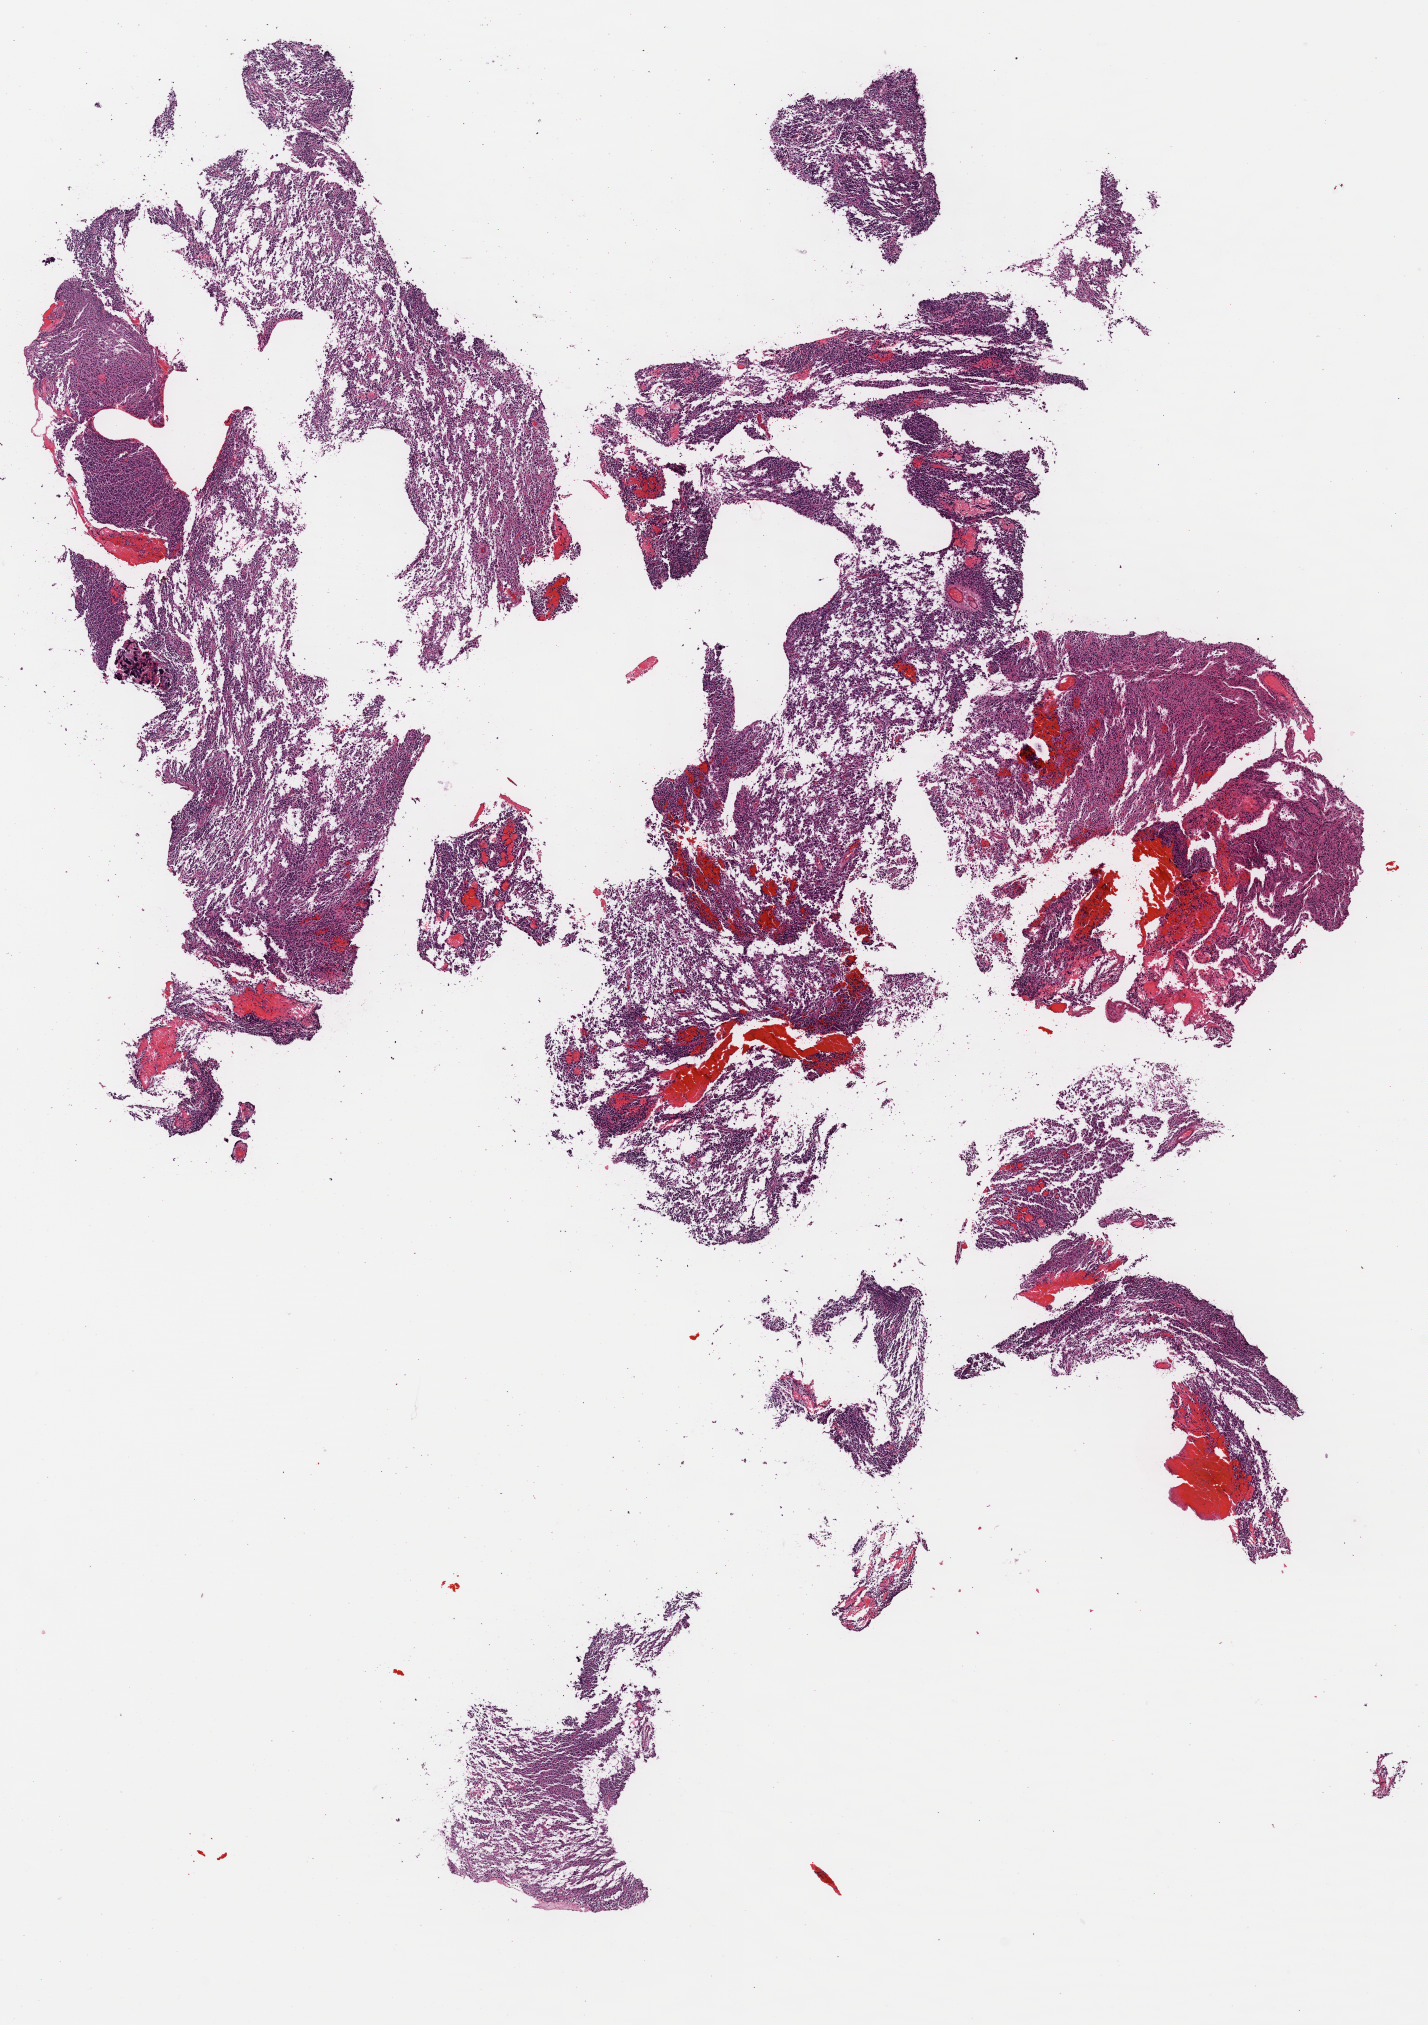
Whole-slide histology image, Hematoxylin and eosin (H&E) stained — whole scanned area (about 11.2 x 15.9 mm, slide scanned at 40x) shown as a low-resolution overview; formalin-fixed paraffin-embedded (FFPE) diagnostic section; primary tumour sample from the brain. Male patient; age at initial diagnosis 29 years. Histologic grade: G2 (moderately differentiated).
Diagnosis: Mixed glioma (cerebrum).